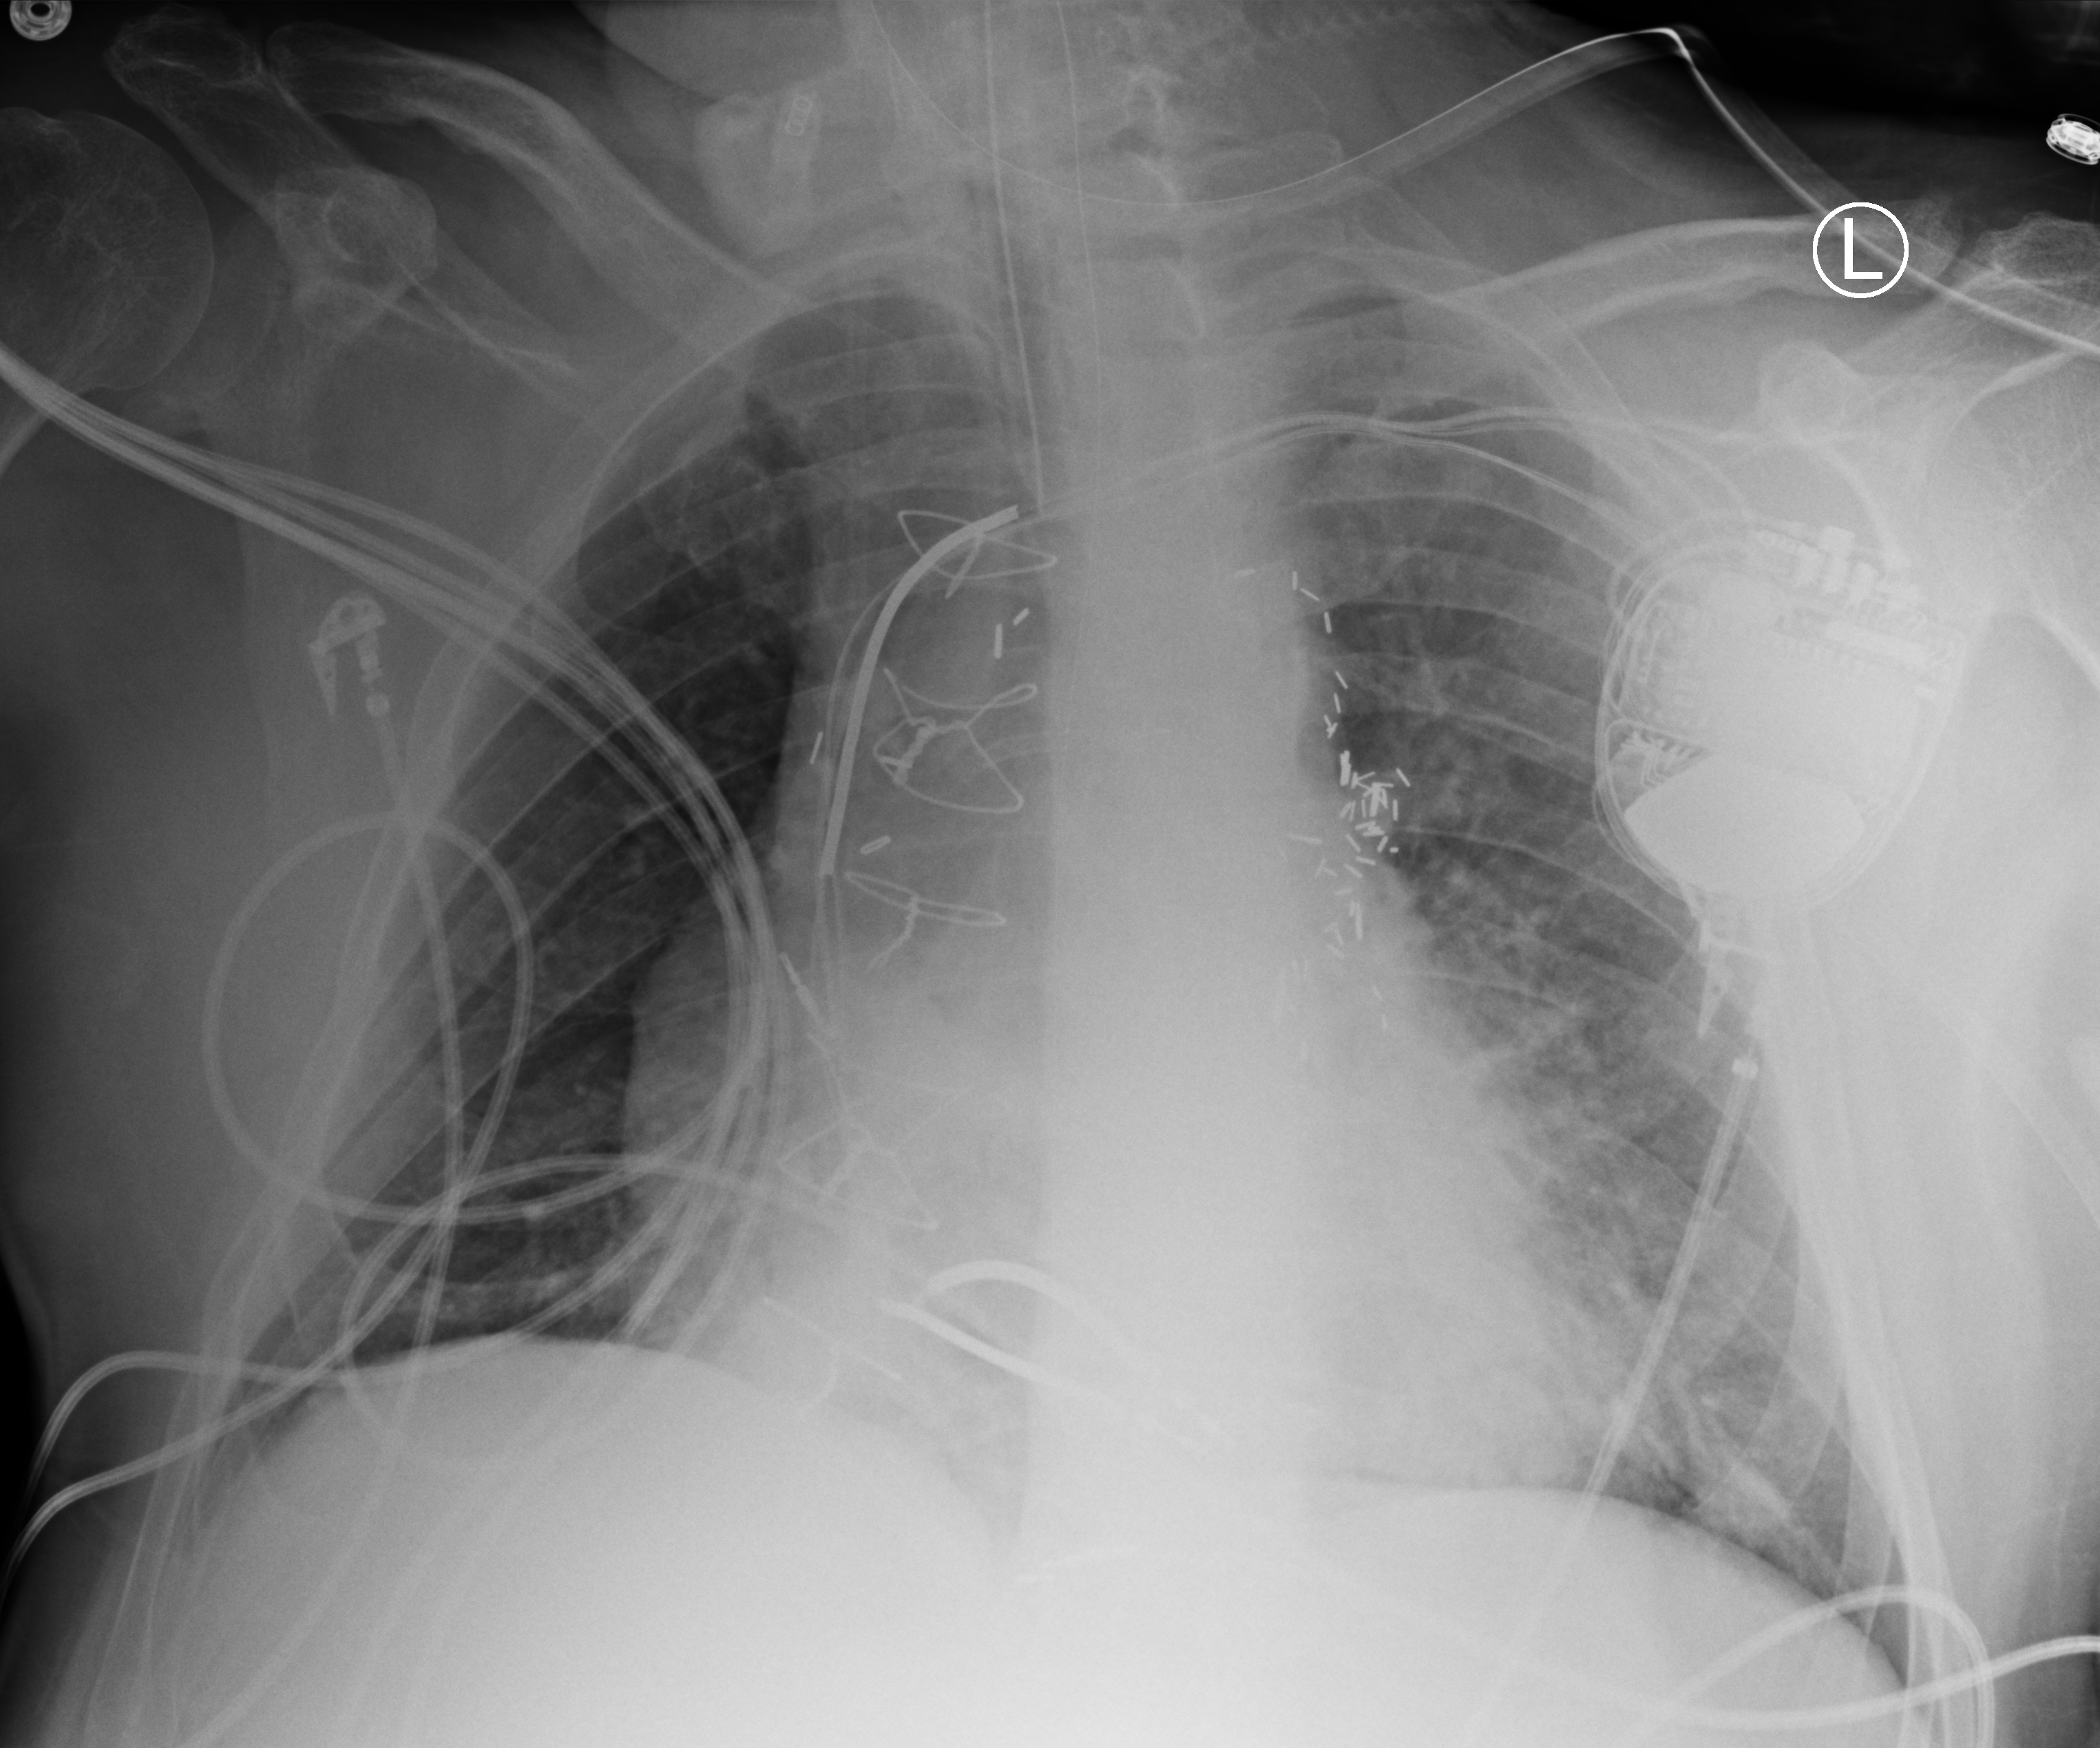
Chest X-ray (portable), anteroposterior (AP) projection. Male patient hospitalised with COVID-19, age 60–74 years.
Admission-level facts for this patient (not findings on this image; timing relative to this image not recorded):
- mechanically ventilated during this hospital stay: yes
- diabetes (admission record): yes
- length of hospital stay: 55 days